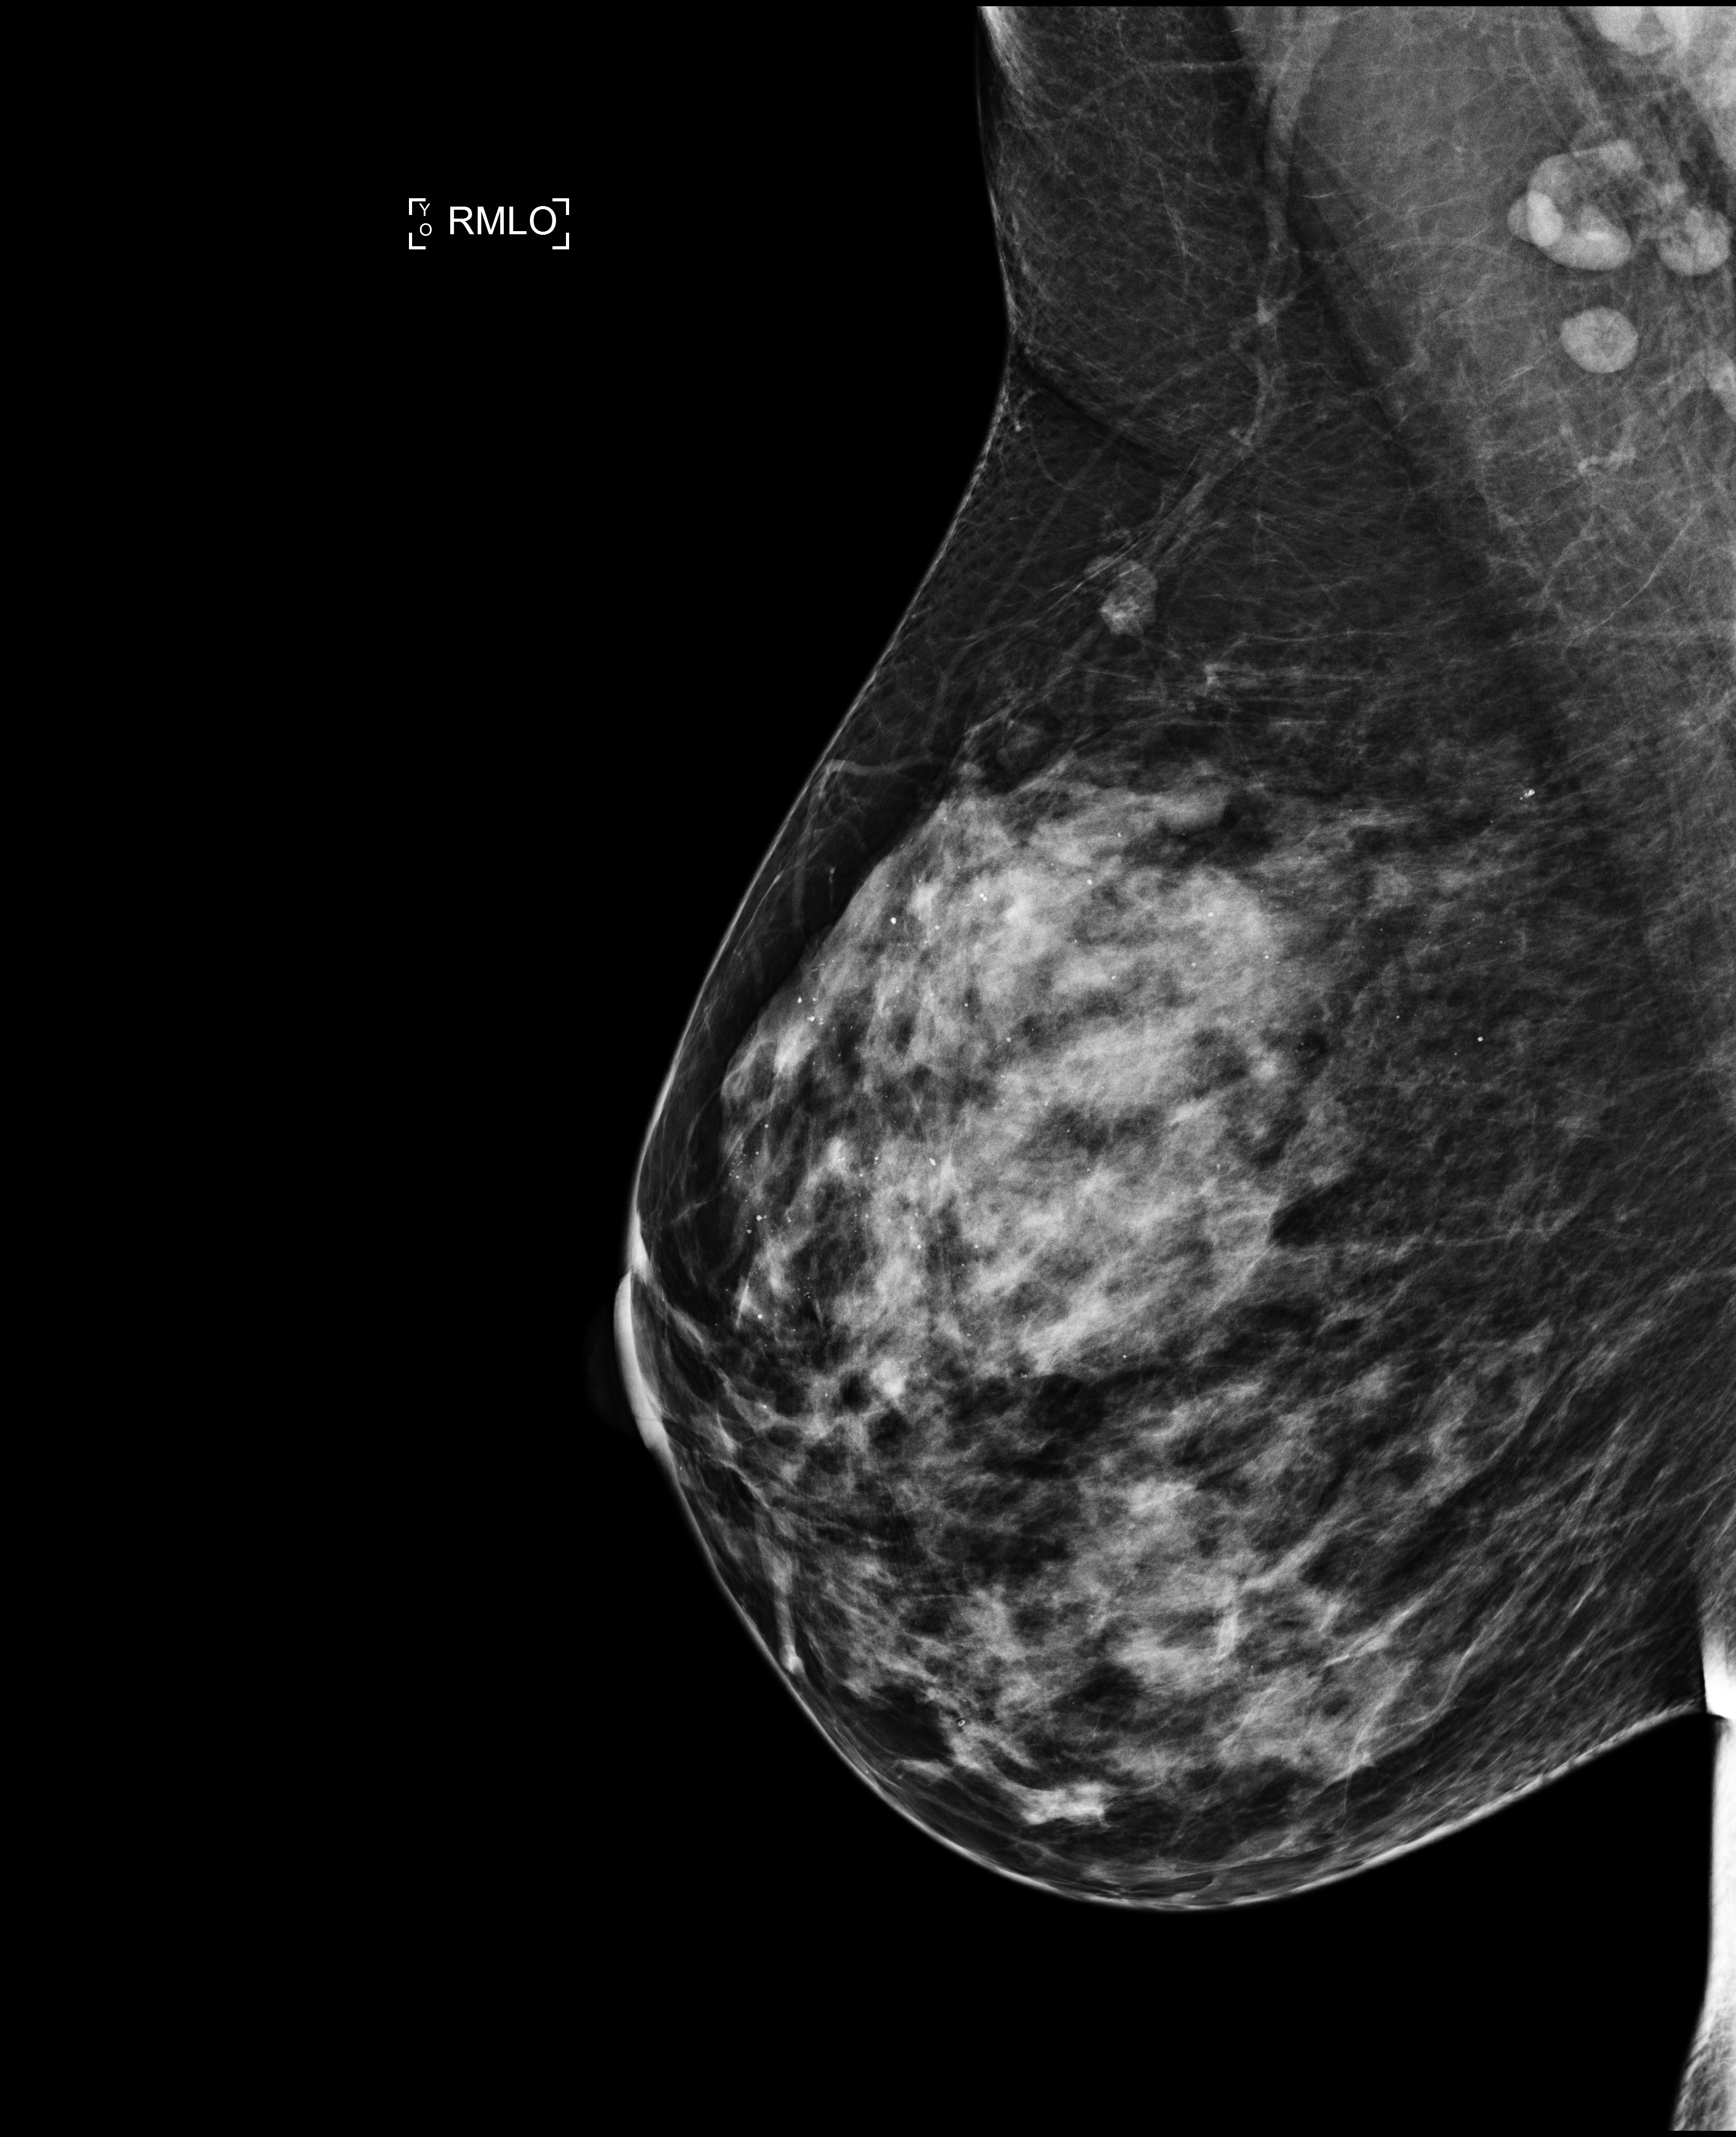
Screening examination; compressed breast thickness 73 mm. Female patient, age 46 years.
Image type: full-field digital mammogram. Breast: right. Projection: mediolateral oblique (MLO) view.